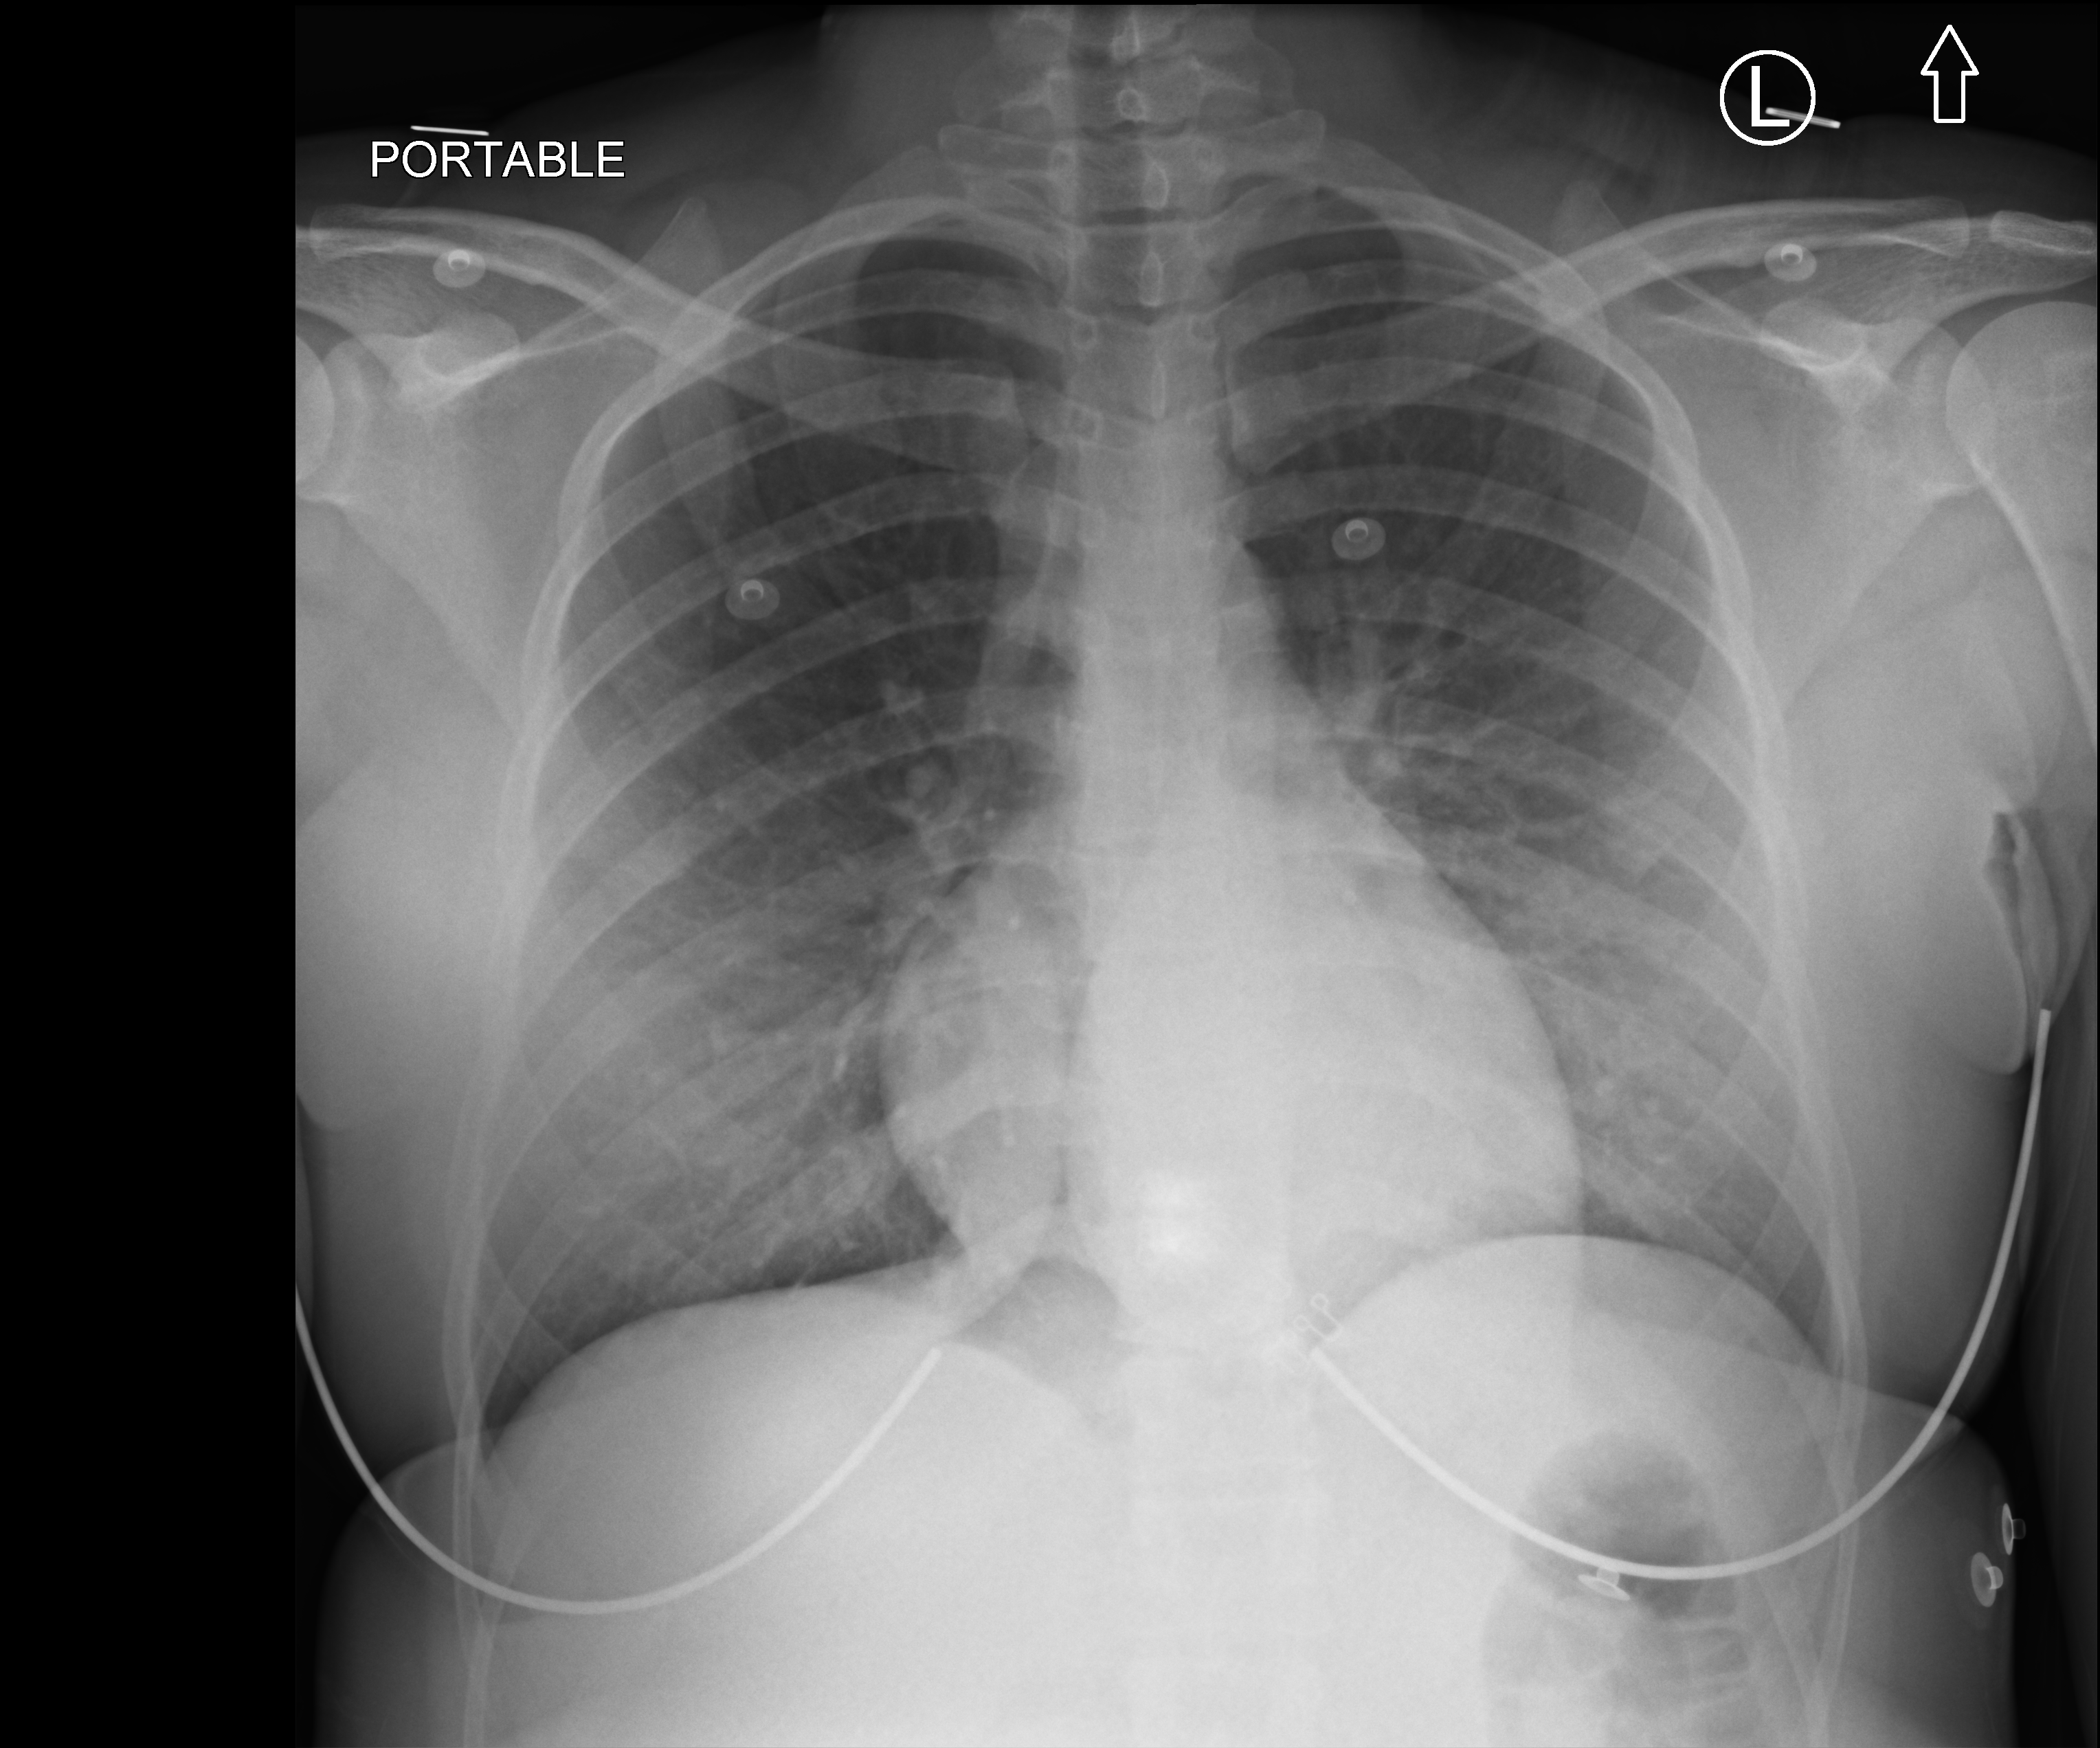
Portable chest radiograph, anteroposterior (AP) projection. Female patient hospitalised with COVID-19, age 18–59 years.
Hospital-stay facts (about this admission, not read from this image; timing relative to this image not recorded):
- length of hospital stay: 2 days